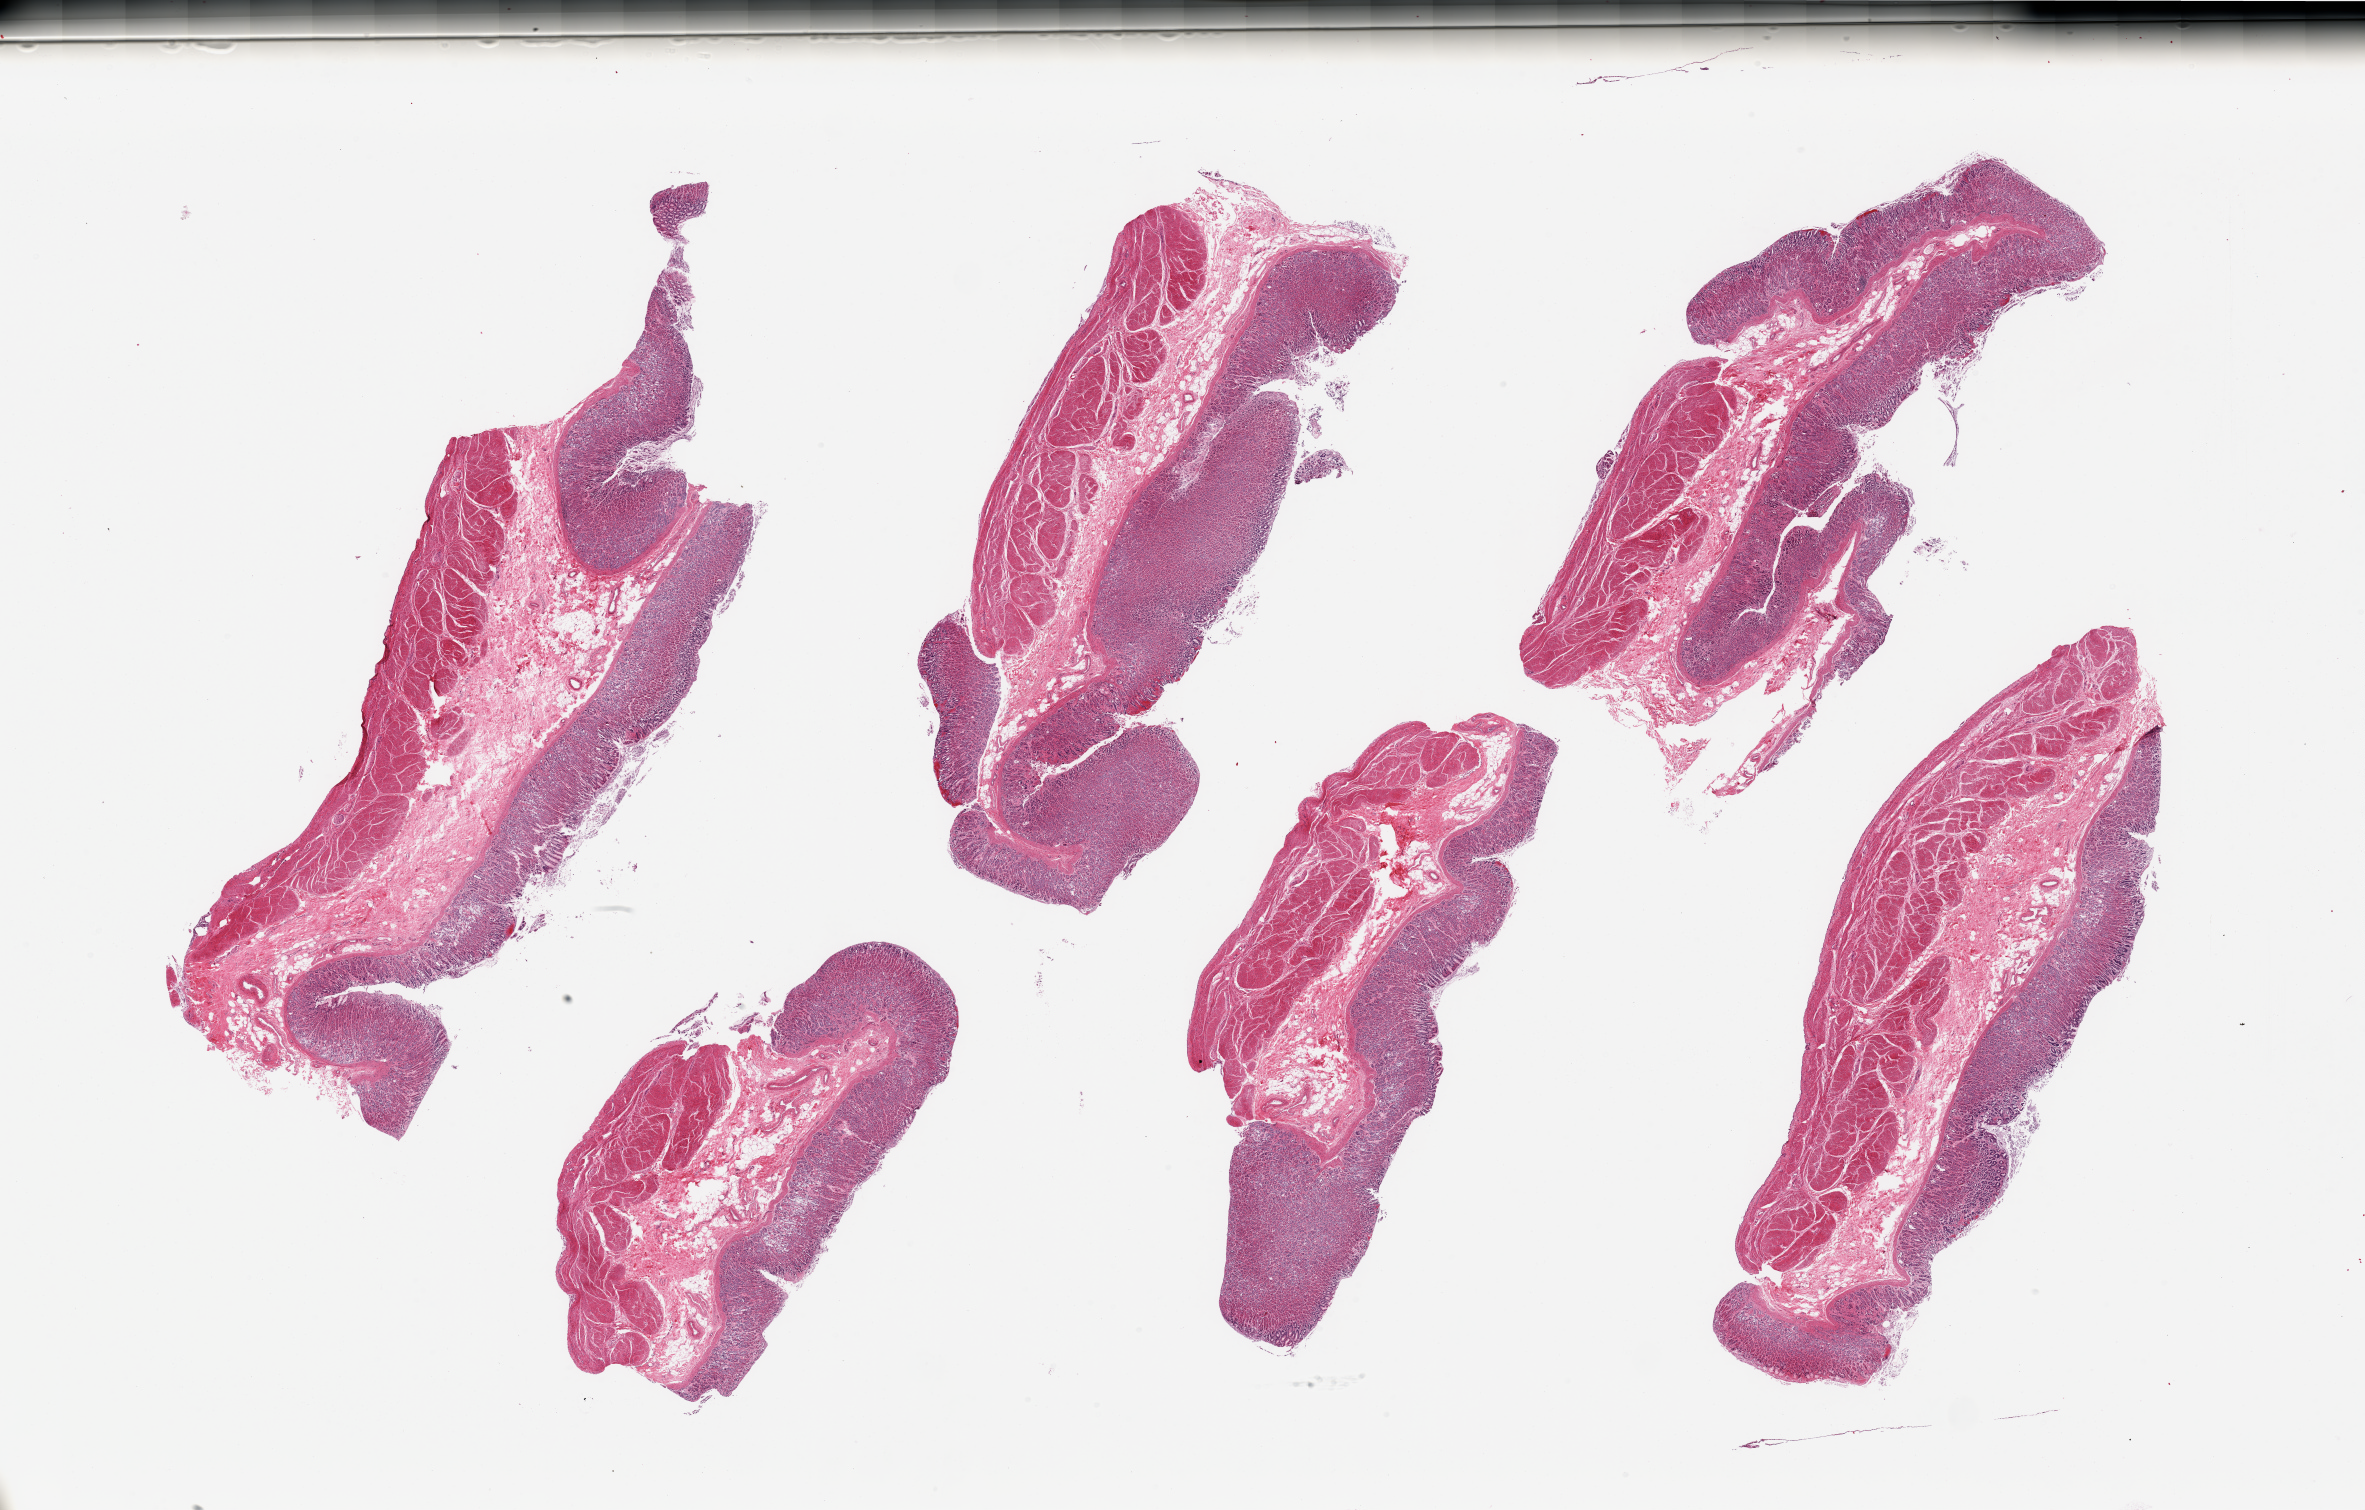
Whole-slide image, haematoxylin and eosin stain — low-resolution overview of the scanned area, about 37.4 x 23.9 mm, PAXgene-fixed, paraffin-embedded tissue, section of stomach (target tissue), tissue donor sample. Male donor.
Review note (as recorded): 6 pieces, gastric mucosa is ~1mm, 25-30% thickness, reasonably well -preserved.